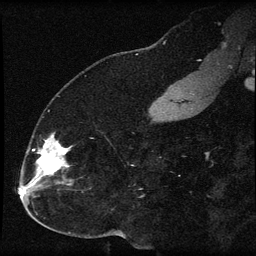
Breast MRI (dynamic contrast-enhanced), one sagittal slice. Position 26 of 60 along the scan axis. Dynamic contrast-enhanced series, image 2 of 3 at this slice position (ordered by acquisition). 1.5 T. TE 4.2 ms, TR 8.2 ms. 2 mm slice thickness. 256 × 256 image matrix, field of view 180 × 180 mm. Patient: female, 32 years.
Outlined on this slice (semi-automatically segmented with operator editing):
- analysis volume of interest (the breast-tissue region the enhancement analysis was run in; not a lesion): box from (x=31, y=134) to (x=73, y=184) px
- tumour enhancement mask (voxels above the 70 % enhancement threshold inside the analysis volume of interest): (x=31, y=134)–(x=71, y=184)